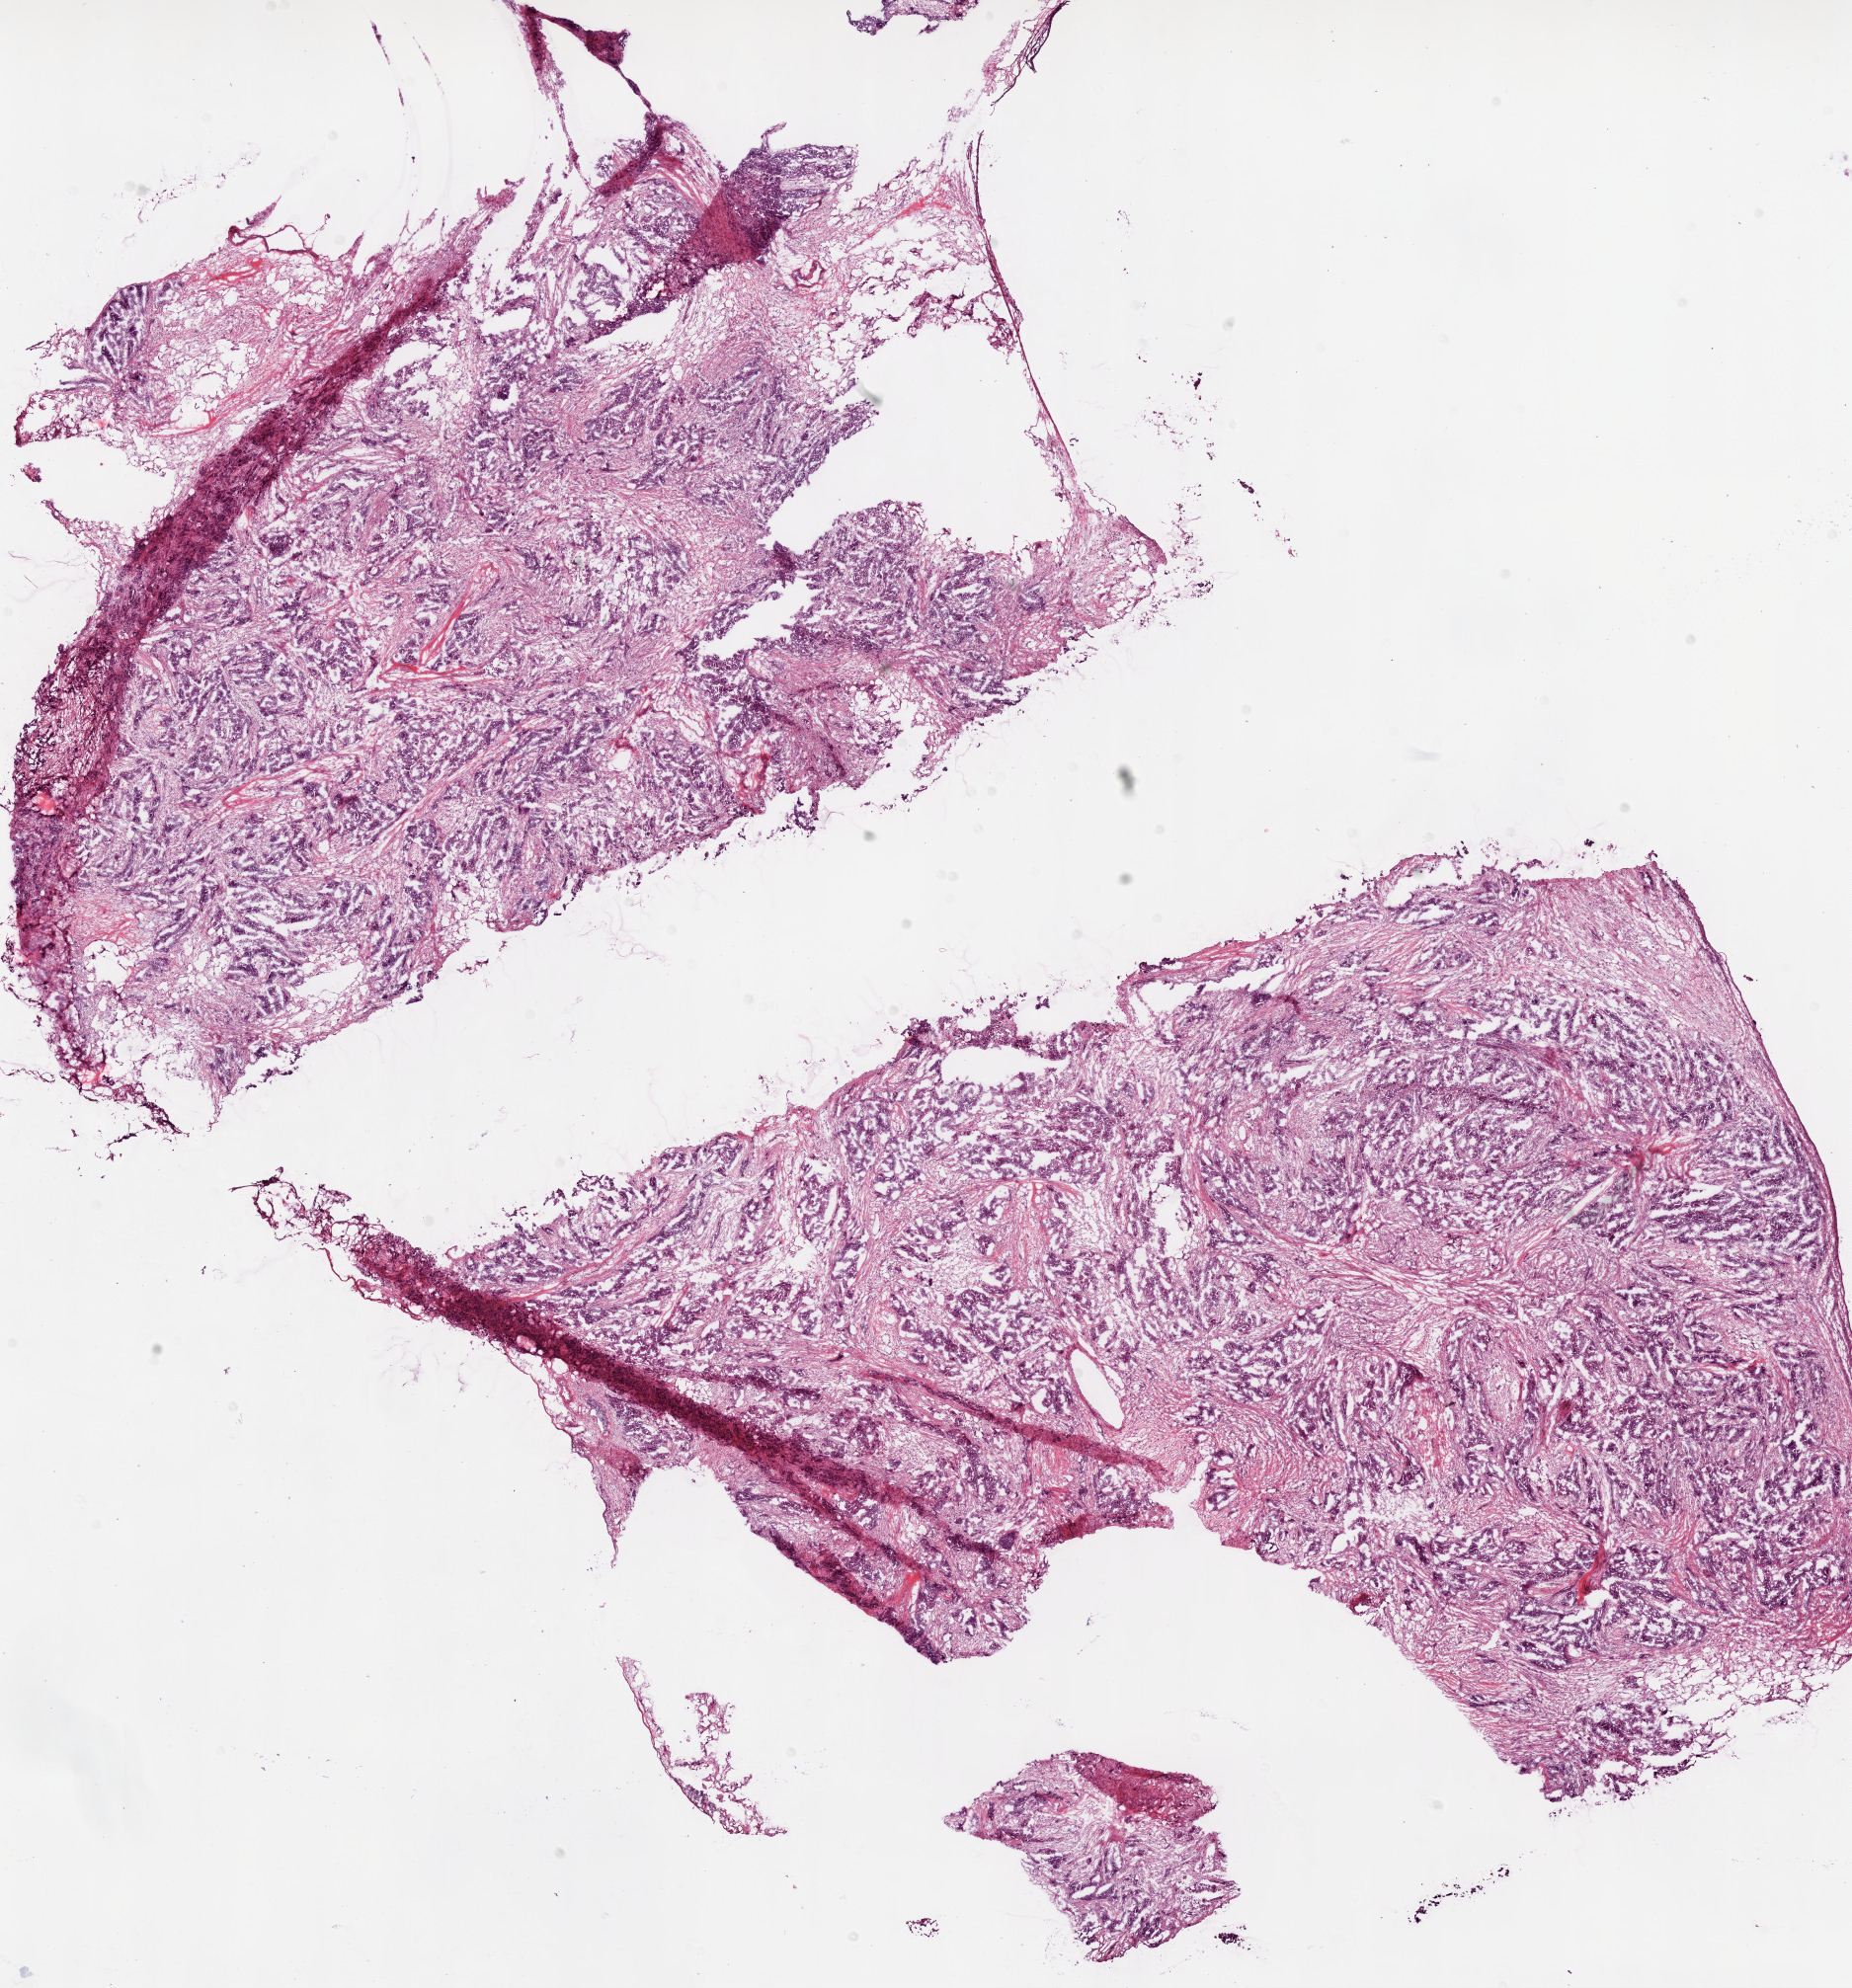
Digitized H&E tissue section (whole slide) — whole scanned area (about 15.0 x 16.2 mm, acquisition: 20x scan) shown as a low-resolution overview. Frozen section from the bottom of the tissue portion. Ovary, primary tumour sample. Patient: female, age at initial diagnosis 50 years. Histologic grade: G3 (poorly differentiated). Slide review estimates, as recorded: tumour cells 69%, tumour nuclei 70%, normal cells 0%, stromal cells 30%, necrosis 1%.
Laterality: bilateral. Diagnosis: Serous cystadenocarcinoma, NOS. FIGO stage: IV.